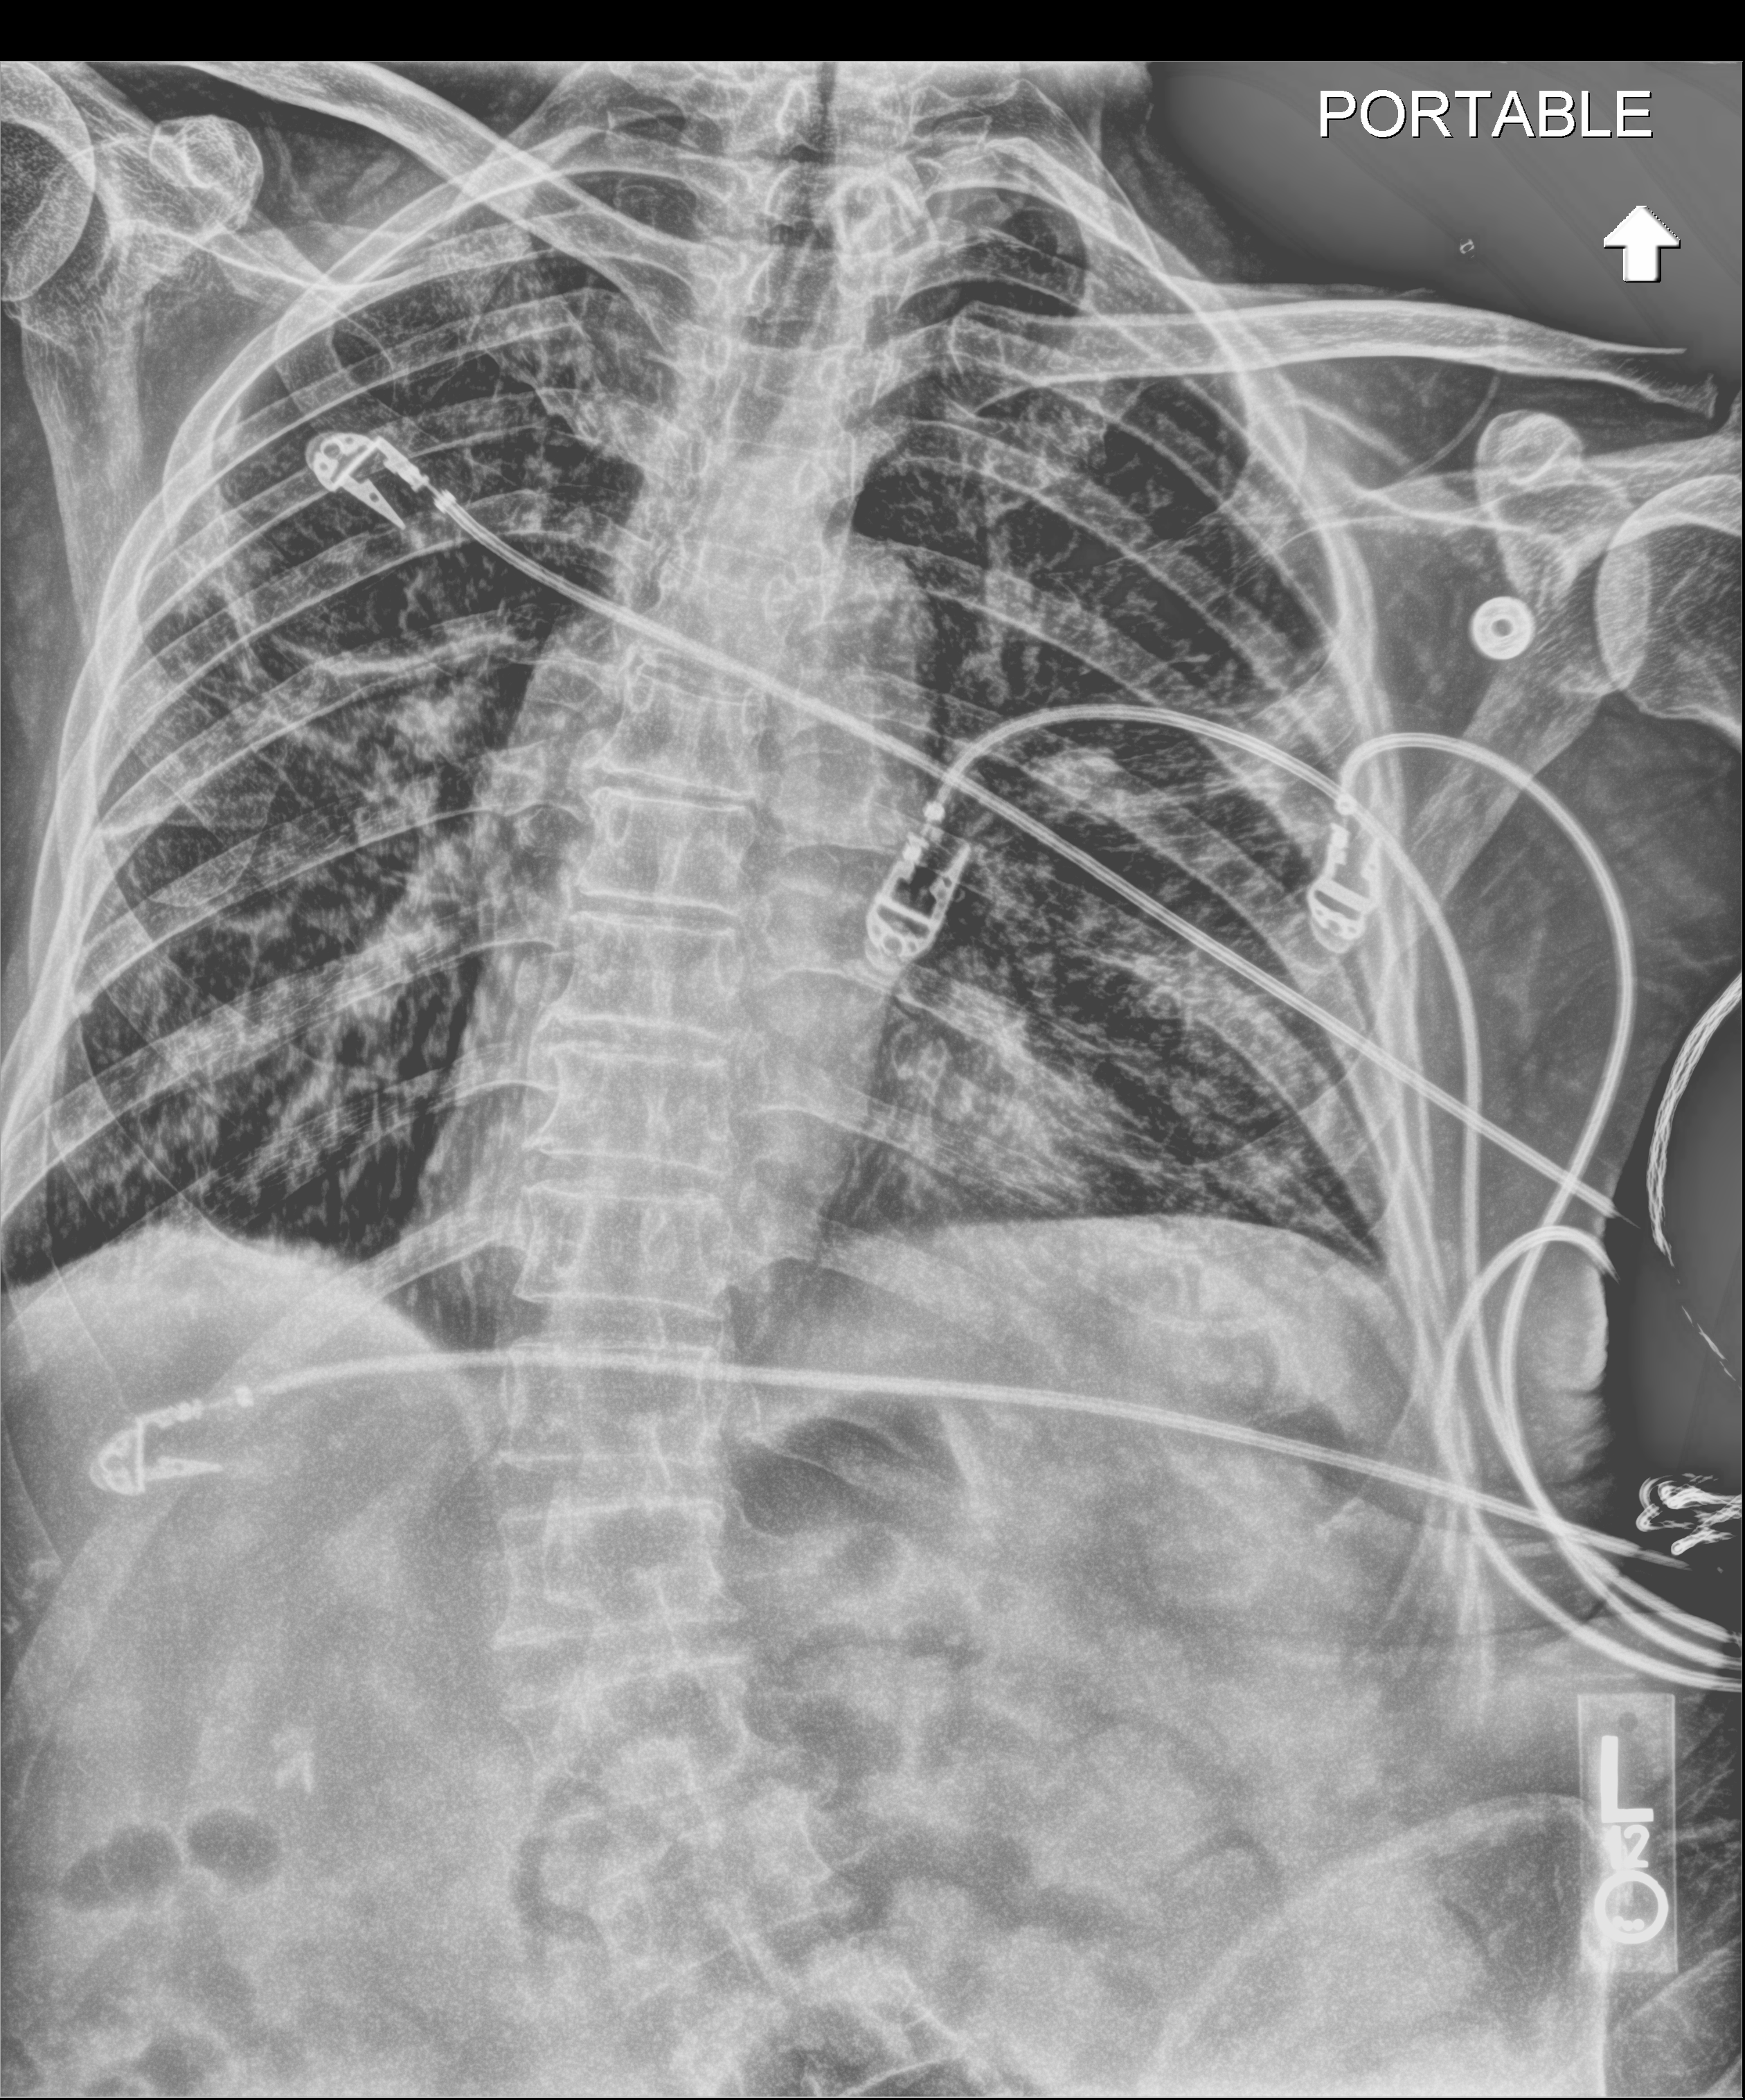
Abdomen radiograph (digital radiography), anteroposterior (AP) projection. Patient hospitalised with COVID-19; male, aged 75–90 years.
Admission-level facts for this patient (not findings on this image; timing relative to this image not recorded): admitted to intensive care during this hospital stay: yes.